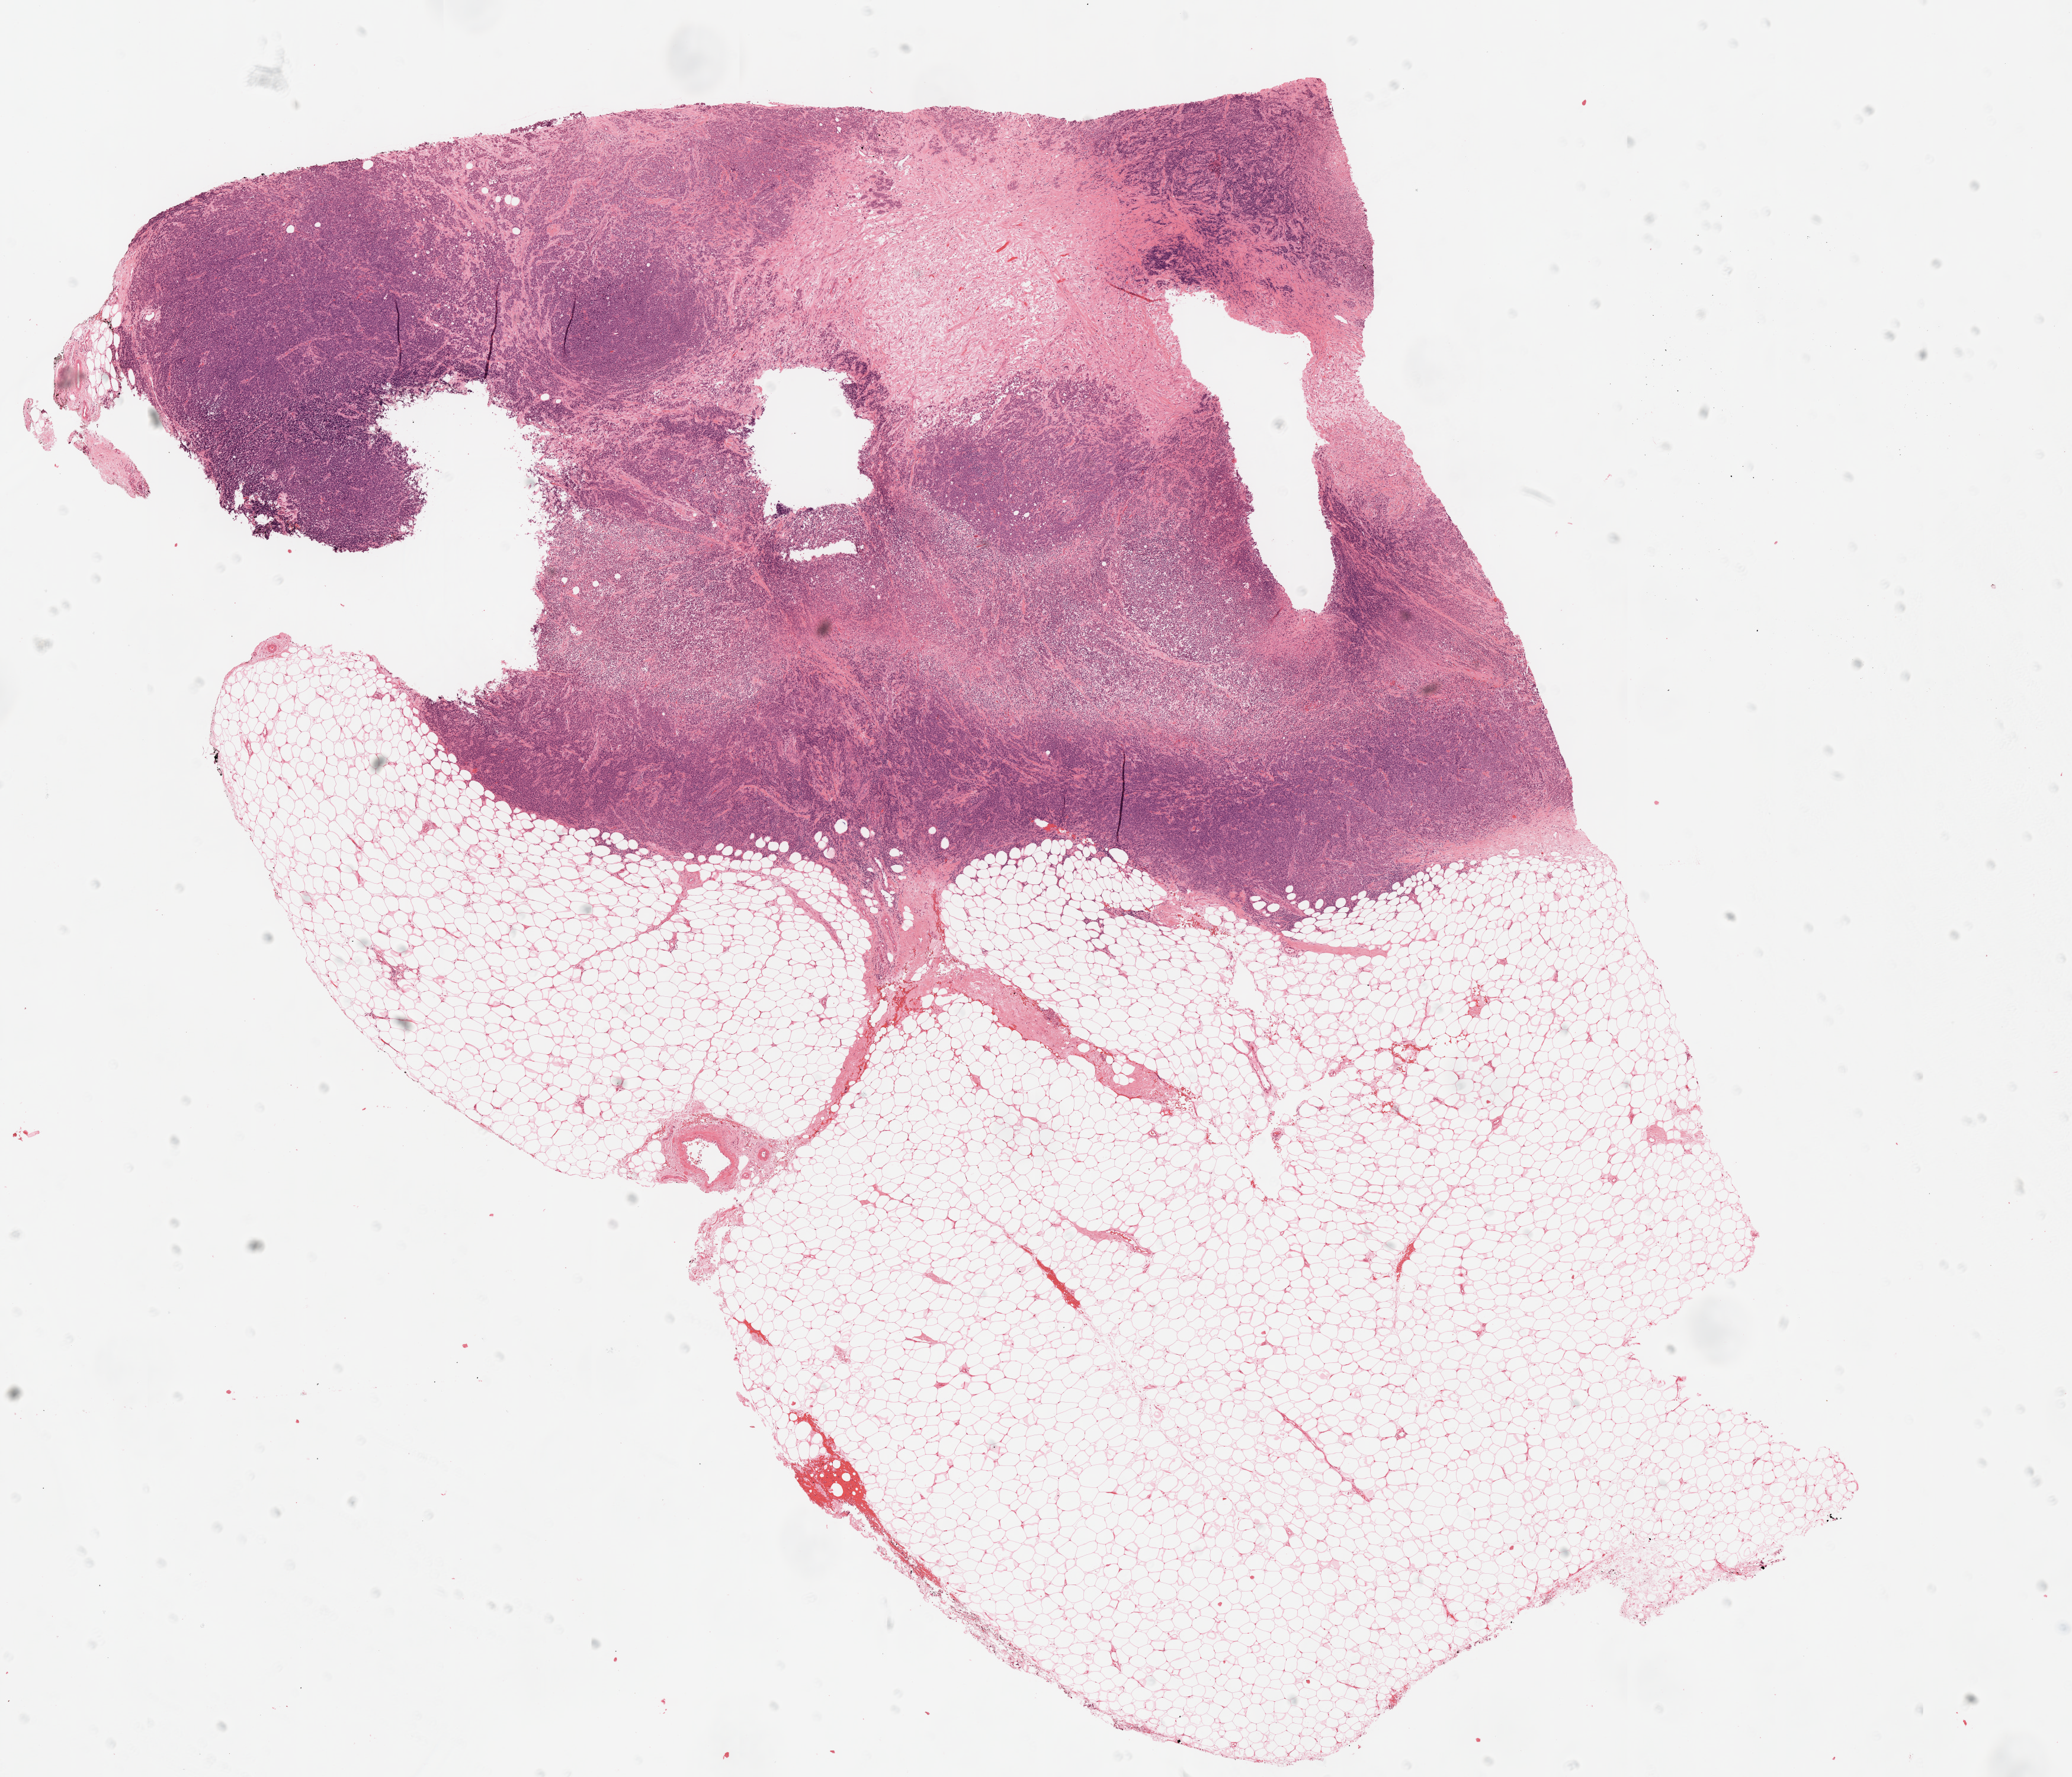
Digitized H&E tissue section (whole slide), whole scanned area (about 14.0 x 12.0 mm) shown as a low-resolution overview. Formalin-fixed paraffin-embedded (FFPE) diagnostic section. Sample: primary tumour, breast. Patient: female, age at initial diagnosis 56 years.
AJCC pathologic stage: IIA. Diagnosis: Lobular carcinoma, NOS. Laterality: left. TNM: T2 N0 M0.